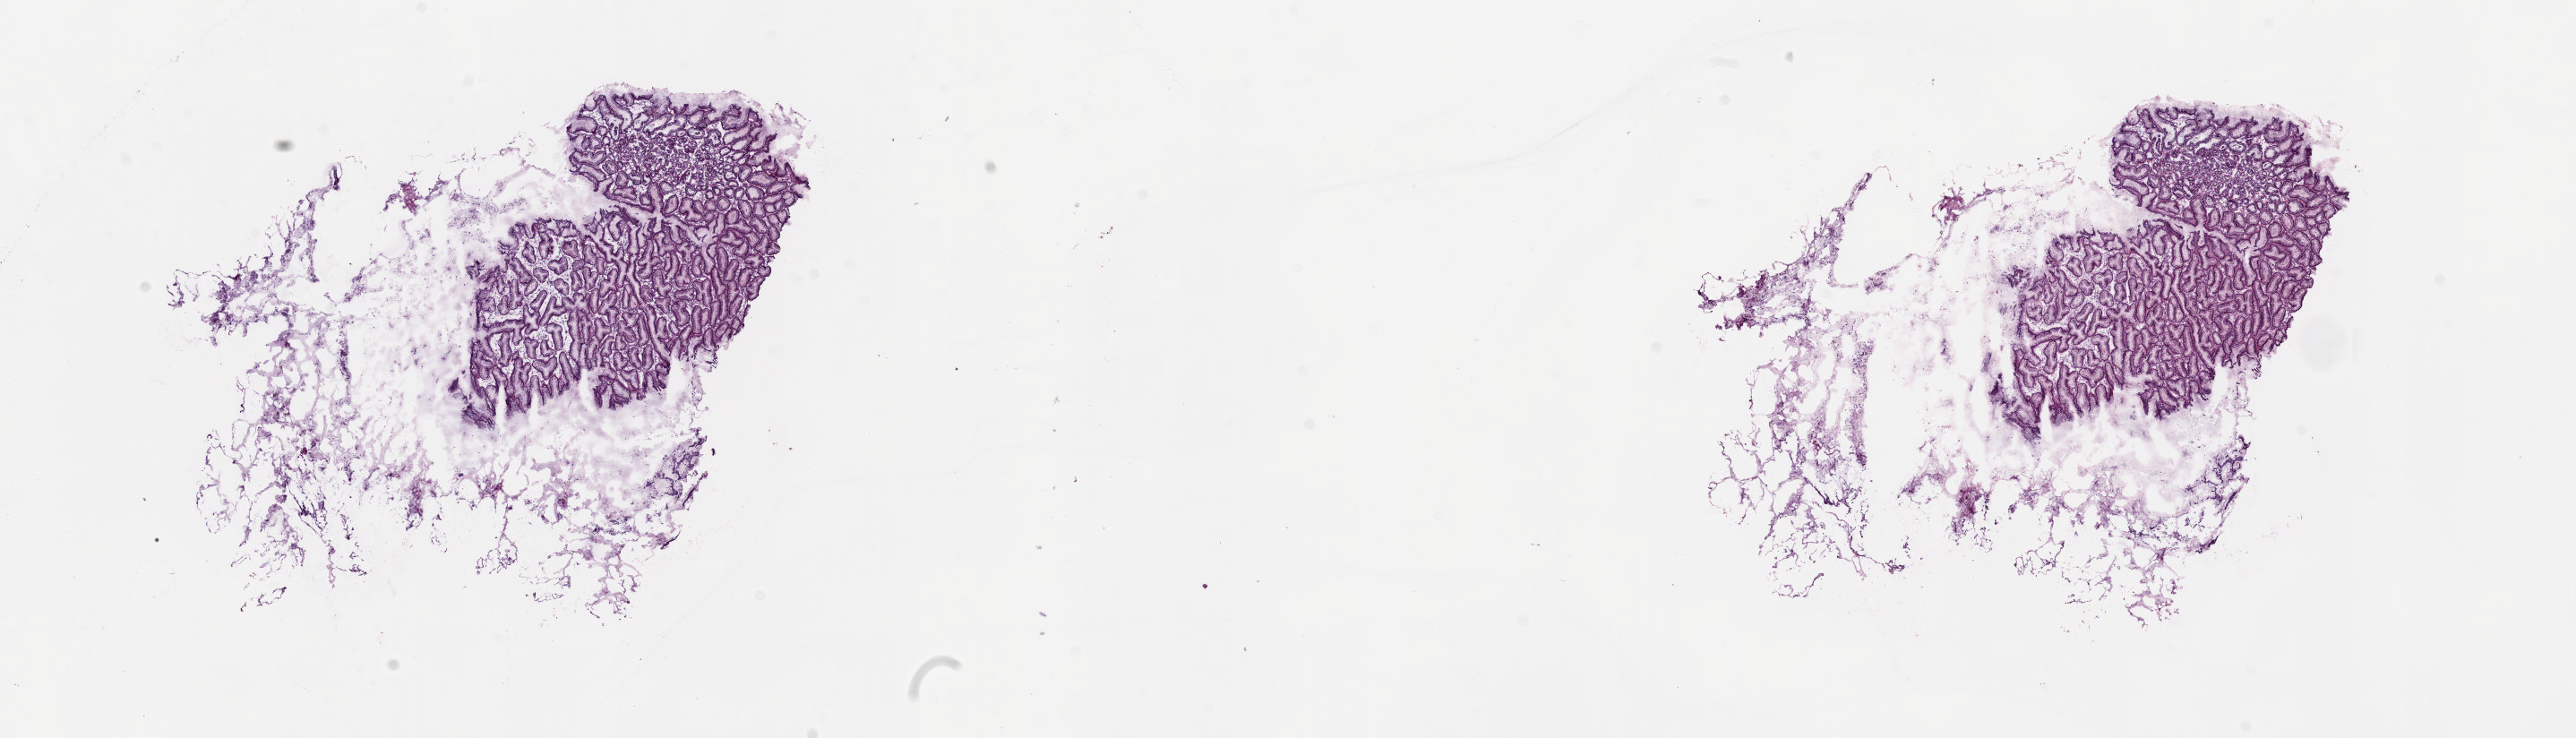
H&E-stained whole-slide image, shown as a low-resolution overview of the whole scanned area (about 22.8 x 6.5 mm), frozen section from the top of the tissue portion, sample: solid tissue normal (non-tumour tissue), esophagus. Female, age 81 years at initial diagnosis. Pathologist review of this section (percent, as recorded): tumour cells 0%, tumour nuclei 0%, normal cells 100%, stromal cells 0%, necrosis 0%. Inflammatory infiltration, as recorded: lymphocyte infiltration 2%, monocyte infiltration 0%, neutrophil infiltration 0%.
This section: solid tissue normal (non-tumour) sample from the same patient. Patient diagnosis: Adenocarcinoma, NOS (lower third of esophagus).